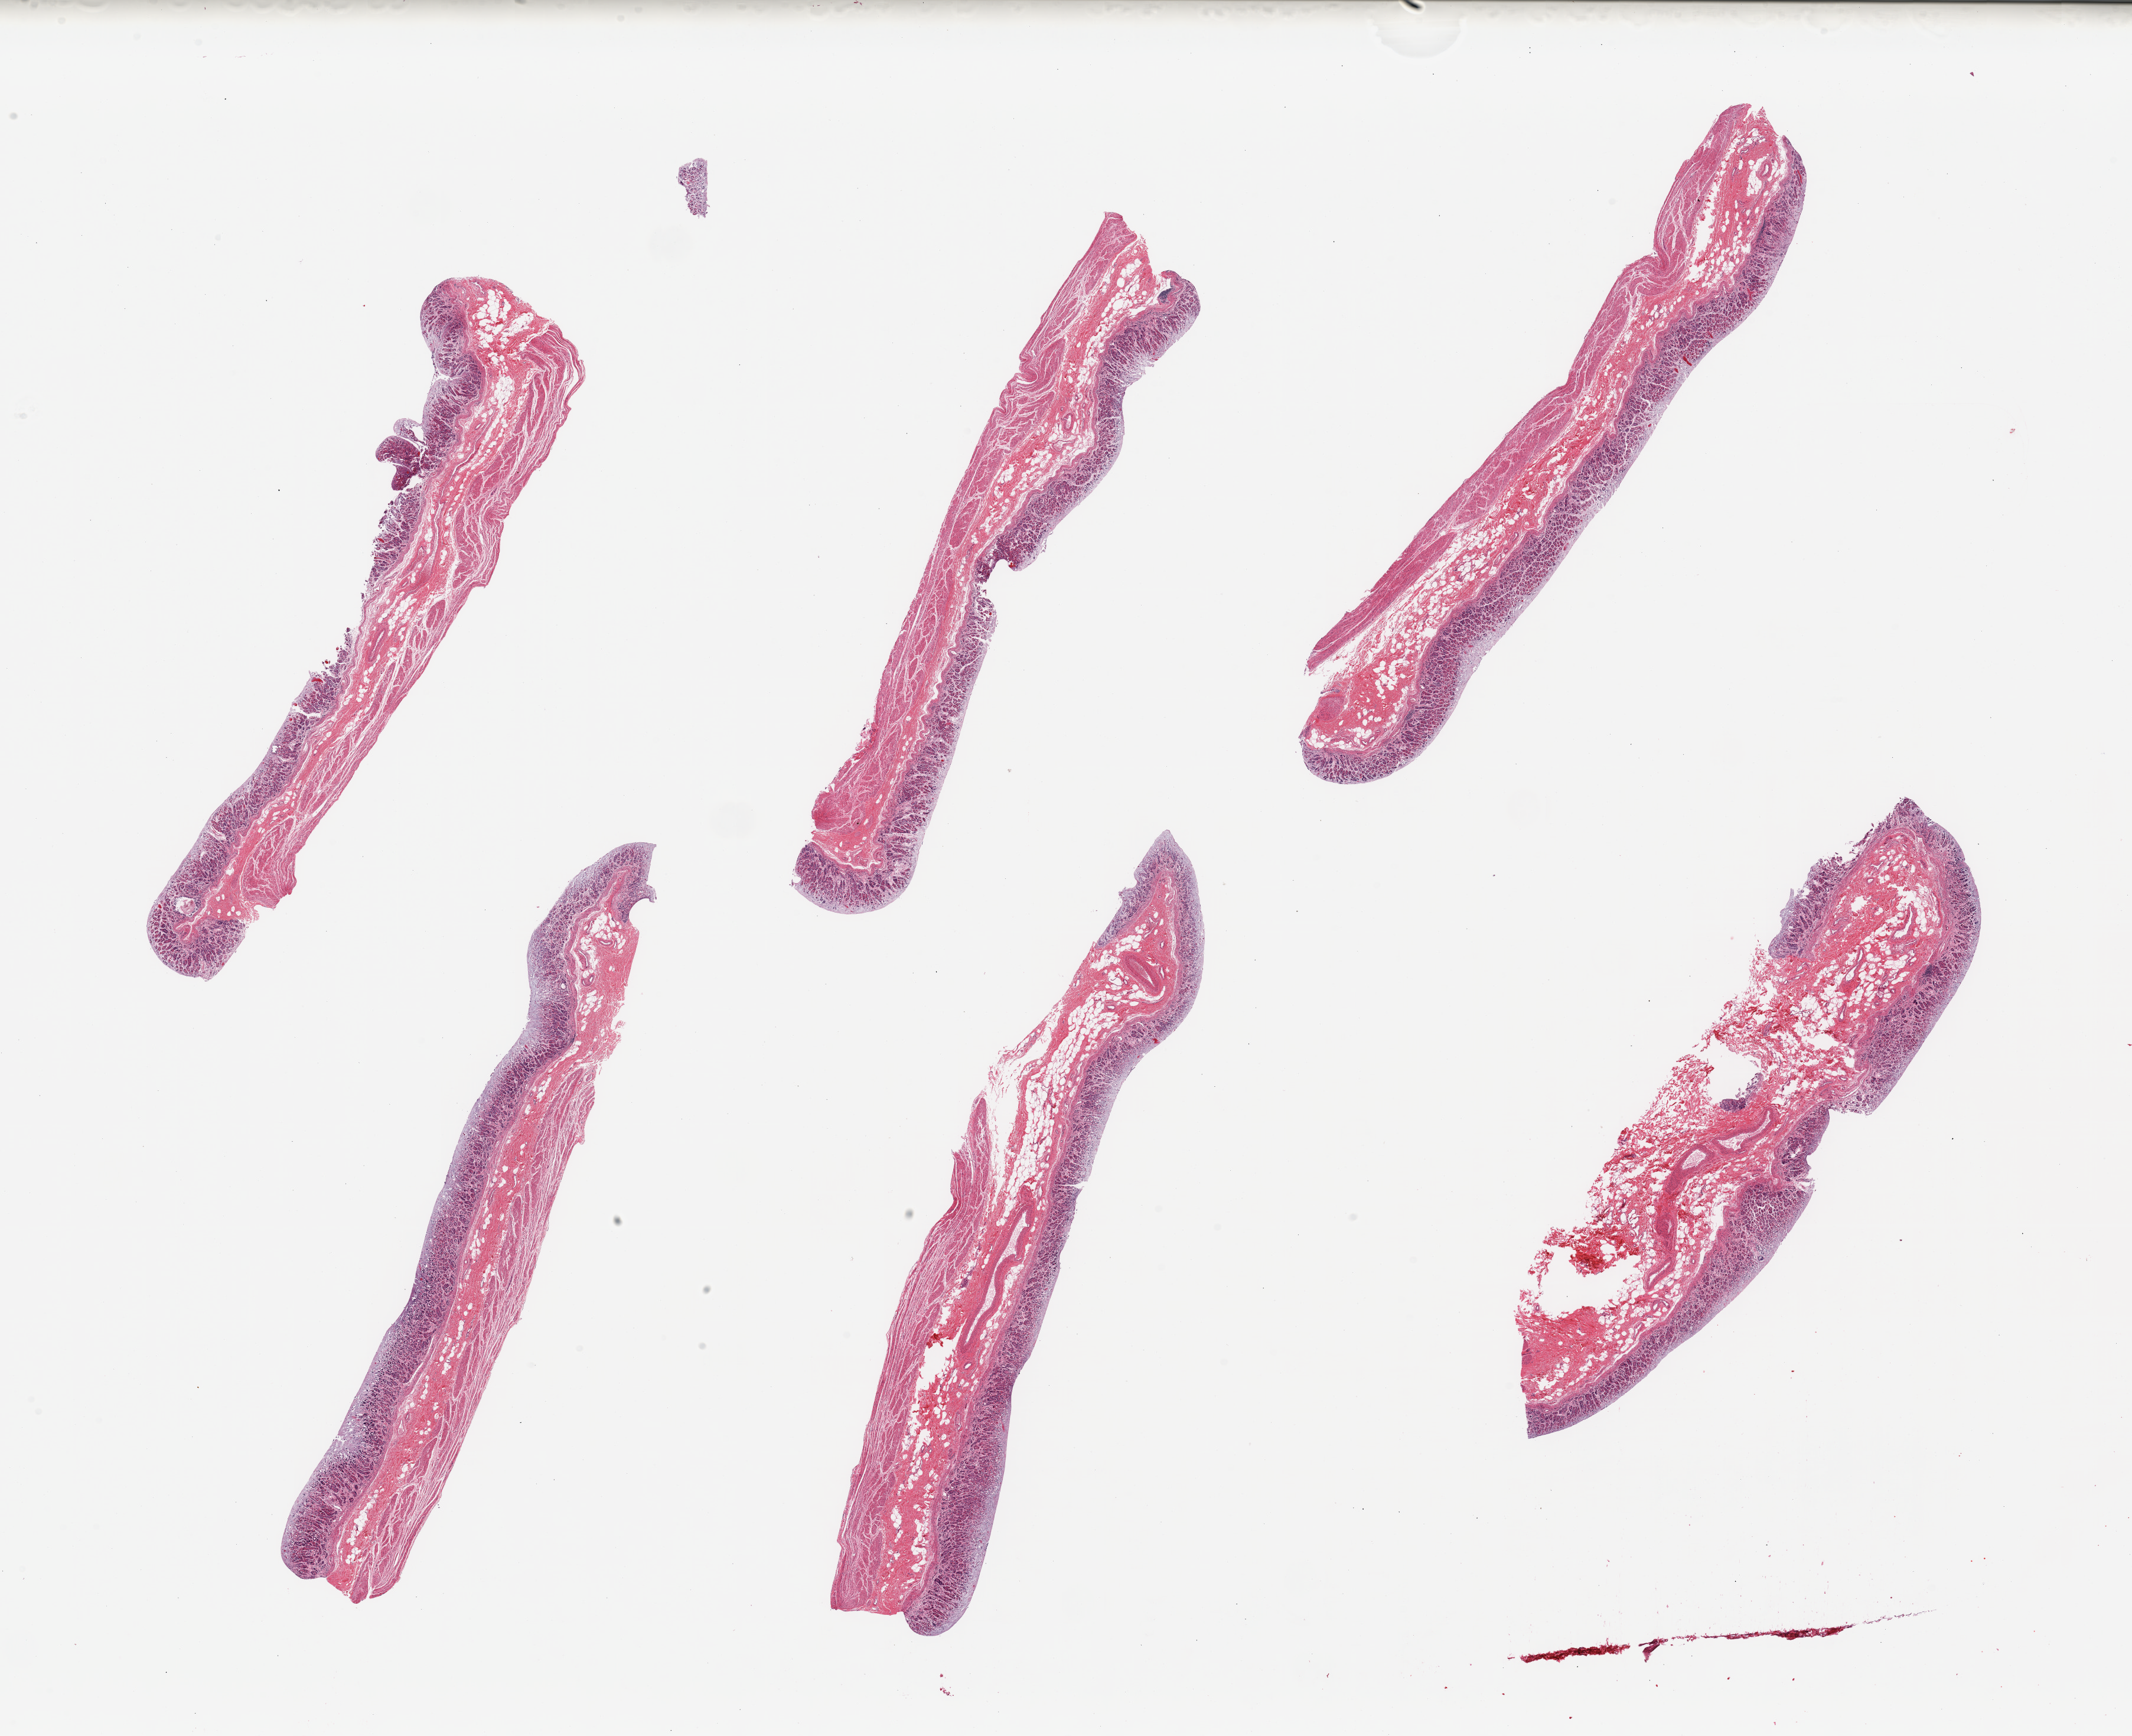
Whole-slide image, hematoxylin and eosin (H&E) stain — a low-resolution overview of the entire scanned area, about 28.5 x 23.2 mm (slide scanned at 20x), PAXgene-fixed, paraffin-embedded tissue, sampled site (target tissue): stomach, donor tissue sample.
Reviewer comment on this tissue sample: 6 pieces; mostly full thickness sections, mucosa is moderately to severely autolyzed.